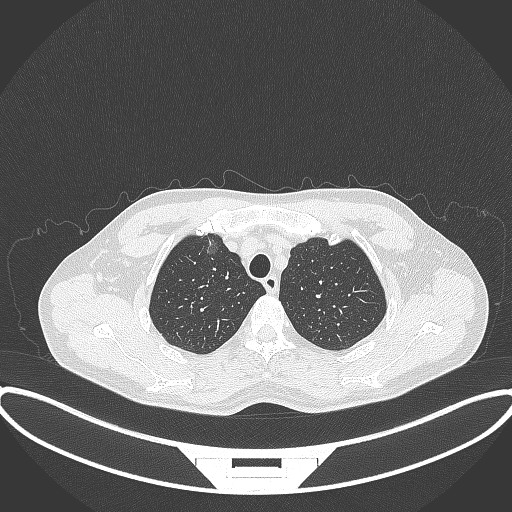
Chest CT, one axial slice; slice 306 of 395 in the series (ordered by position); 120 kVp; lung window (W 1500 / L -600 HU); 1 mm slice thickness; 512 × 512 image matrix. Male patient, age 60 years. From the clinical record (not read from this slice): clinical TNM (as recorded): T1c N0 M0.
Structures marked on this image (bounding box drawn by a radiologist):
- lung tumour (recorded histology: adenocarcinoma): bounding box [x1, y1, x2, y2] px = [198, 228, 220, 261]